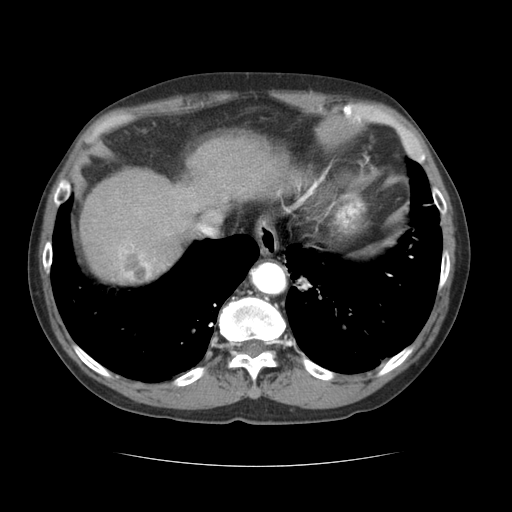
Contrast-enhanced abdominal CT (liver protocol), one axial slice; position 56 of 69 along the scan axis; reconstruction kernel STANDARD; 120 kVp; soft-tissue window (W 400 / L 40 HU); 2.5 mm slice thickness; 512 × 512 image matrix, field of view 360 × 360 mm. Case-level facts recorded for this patient, not image findings: diagnosis: hepatocellular carcinoma (patient treated with transarterial chemoembolisation; whether this scan precedes or follows treatment is not stated here); TNM stage (as recorded): Stage-II; Child-Pugh class: B; tumour differentiation: poorly differentiated; tumour size: 2.6 cm.
Structures marked on this image (semi-automatically segmented with operator editing):
- abdominal aorta: bounding box <252,263,285,294> (left, top, right, bottom; pixels)
- liver parenchyma outside the tumour (the mass and vessels are separate outlines, so this box may not span the whole liver): <80,136,305,282>
- mass: <114,240,161,283>